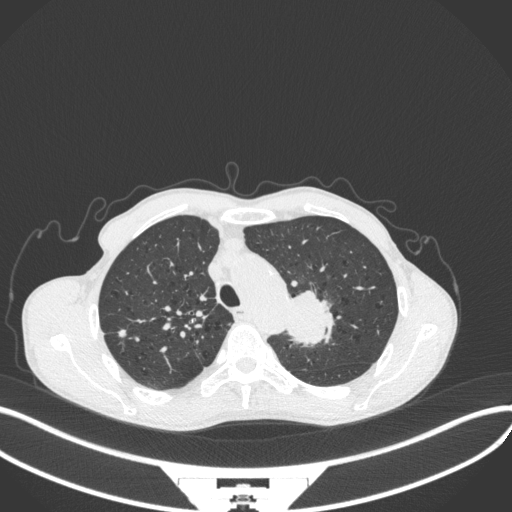
Chest CT, one axial slice; slice 321 of 394 in the series (ordered by position); reconstruction kernel B31f; lung window (W 1500 / L -600 HU); 1 mm slice thickness; 512 × 512 image matrix. Male patient, age 65 years. Case-level facts recorded for this patient, not image findings: clinical TNM (as recorded): T2b N0 M0.
Outlined on this slice (bounding box drawn by a radiologist):
- lung tumour (recorded histology: adenocarcinoma): bounding box [x1, y1, x2, y2] px = [284, 285, 336, 350]